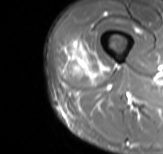
MRI of an extremity soft-tissue mass, one axial slice; slice 17 of 61 in the series (ordered by position); STIR; MR volume resampled by the dataset authors to the PET/CT grid (not the native acquisition matrix); 3.27 mm slice thickness; 163 × 154 image matrix, field of view 159 × 150 mm. Male patient. From the clinical record (not read from this slice): histological type: poorly differentiated synovial sarcoma; grade: high; site of the primary tumour: right buttock.
Annotated regions visible in this slice (expert contour drawn on MRI and transferred to this co-registered scan by the dataset authors):
- gross tumour volume including surrounding oedema: box from (x=66, y=39) to (x=104, y=79) px